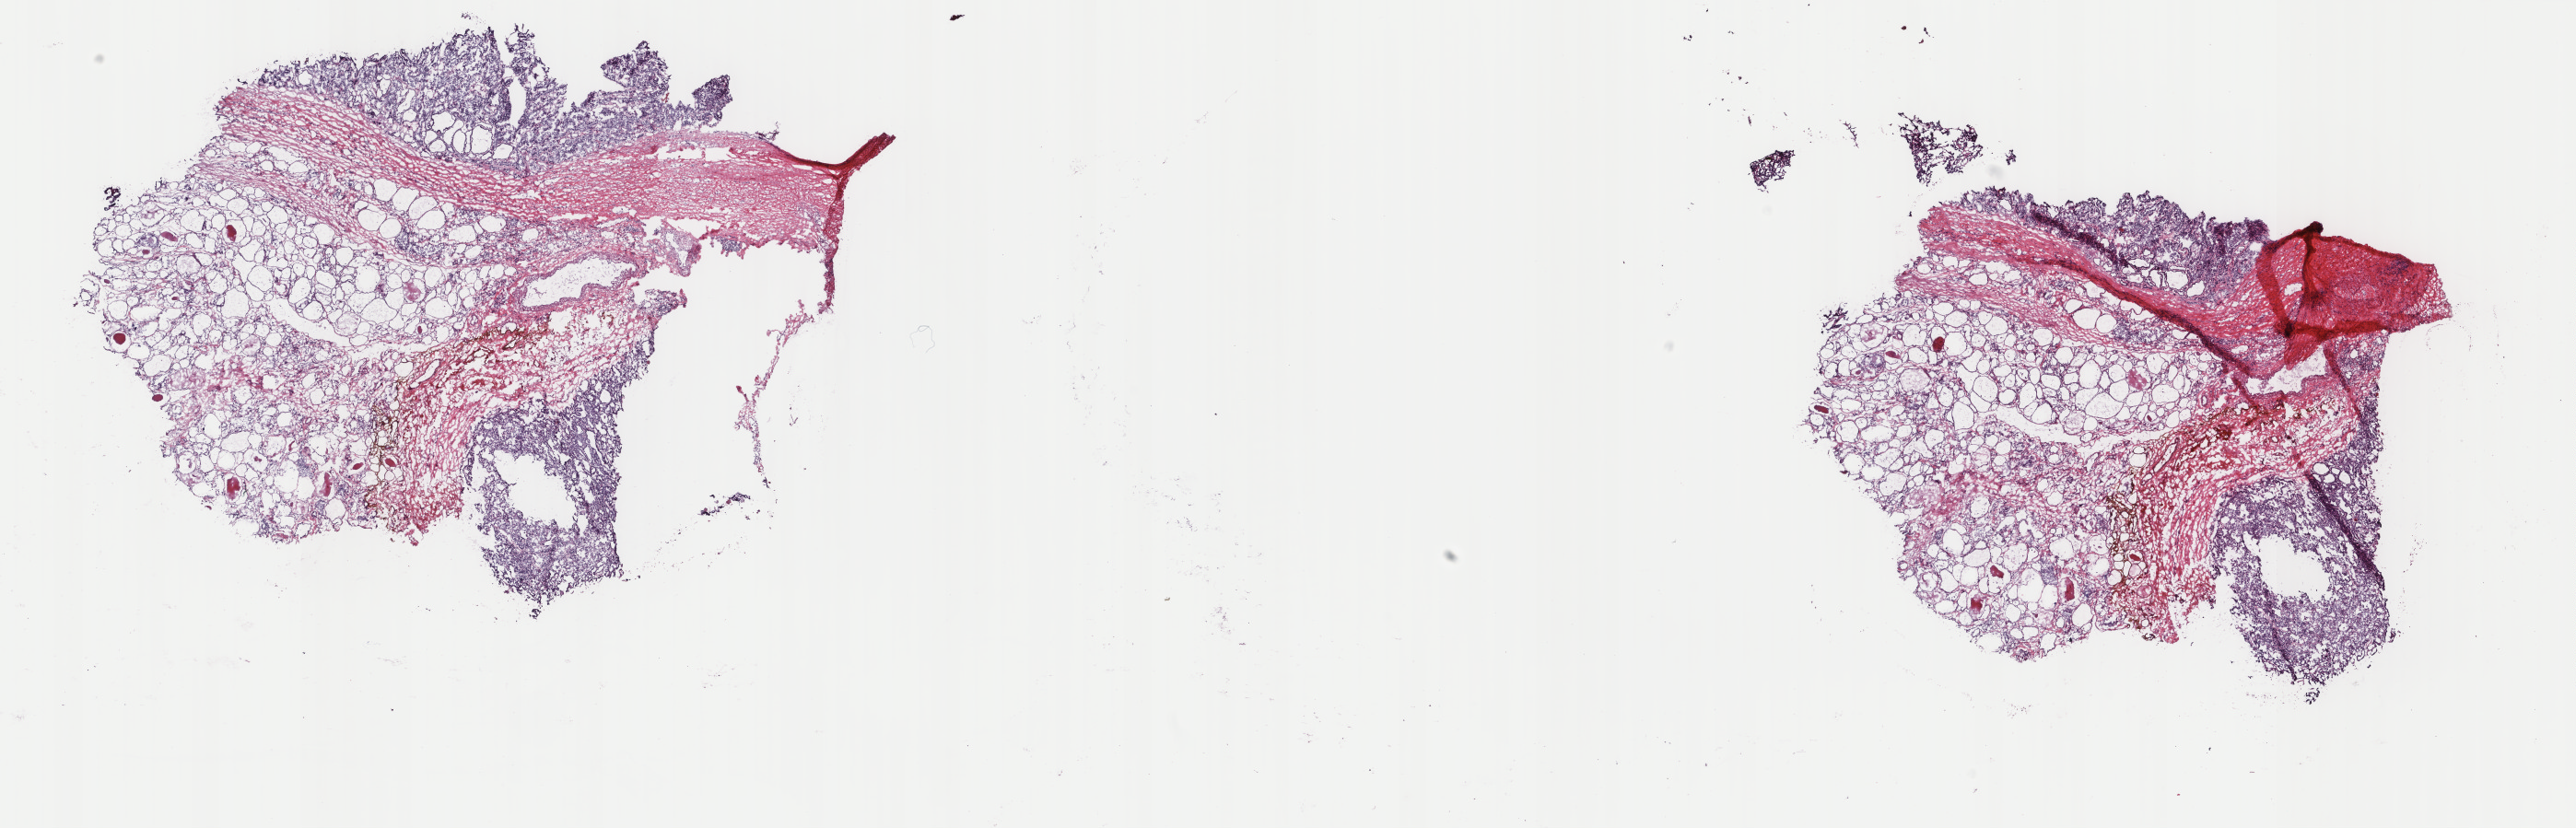
H&E whole-slide image, a low-resolution overview of the entire scanned area, about 22.2 x 7.1 mm (acquisition: 40x scan). Frozen section from the top of the tissue portion. Primary tumour sample from the thyroid. Female, age 55 years at initial diagnosis. Slide review estimates, as recorded: tumour cells 65%, tumour nuclei 65%, normal cells 0%, stromal cells 35%, necrosis 0%. Infiltration values recorded for this section: lymphocyte infiltration 2%, monocyte infiltration 1%, neutrophil infiltration 0%.
TNM: T2 N1a MX. Diagnosis: Papillary adenocarcinoma, NOS (thyroid gland). AJCC pathologic stage: III (7th edition).